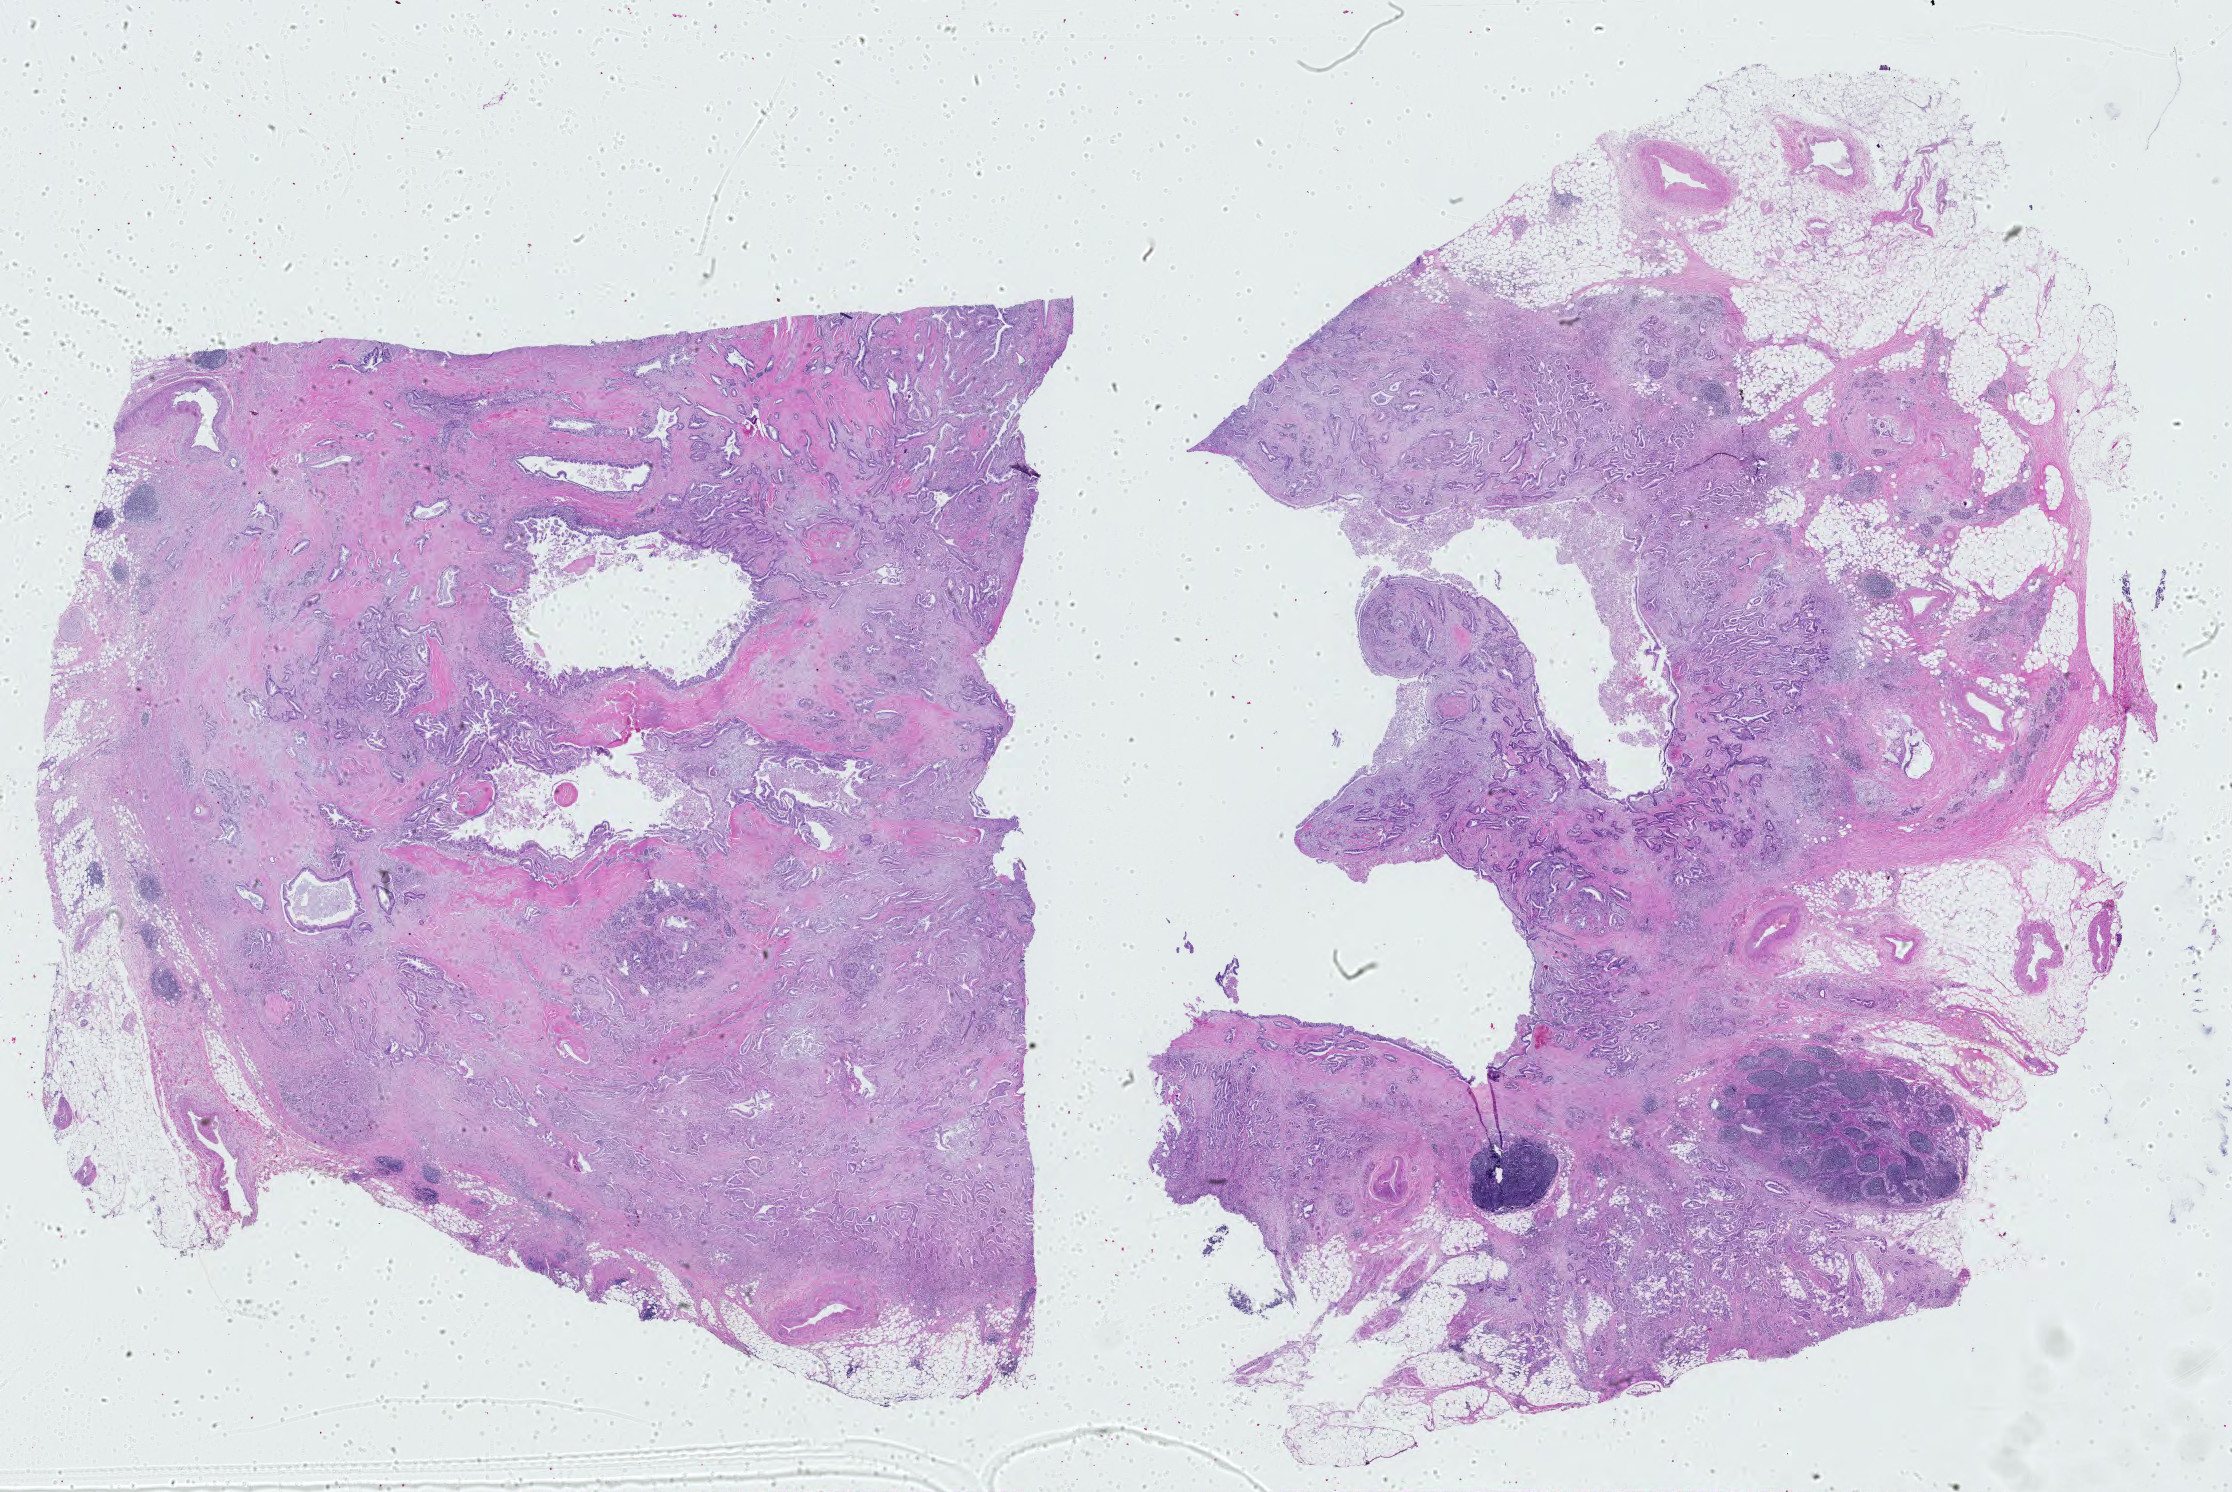
H&E whole-slide image — a low-resolution overview of the entire scanned area, about 32.4 x 21.6 mm, formalin-fixed paraffin-embedded (FFPE) diagnostic section, sample: primary tumour, pancreas. Patient: female, age at initial diagnosis 80 years. Histologic grade: G2 (moderately differentiated).
Pathologic diagnosis: Adenocarcinoma with mixed subtypes. Lymph nodes positive (case pathology): 8 of 24 examined. AJCC pathologic stage: IIB.